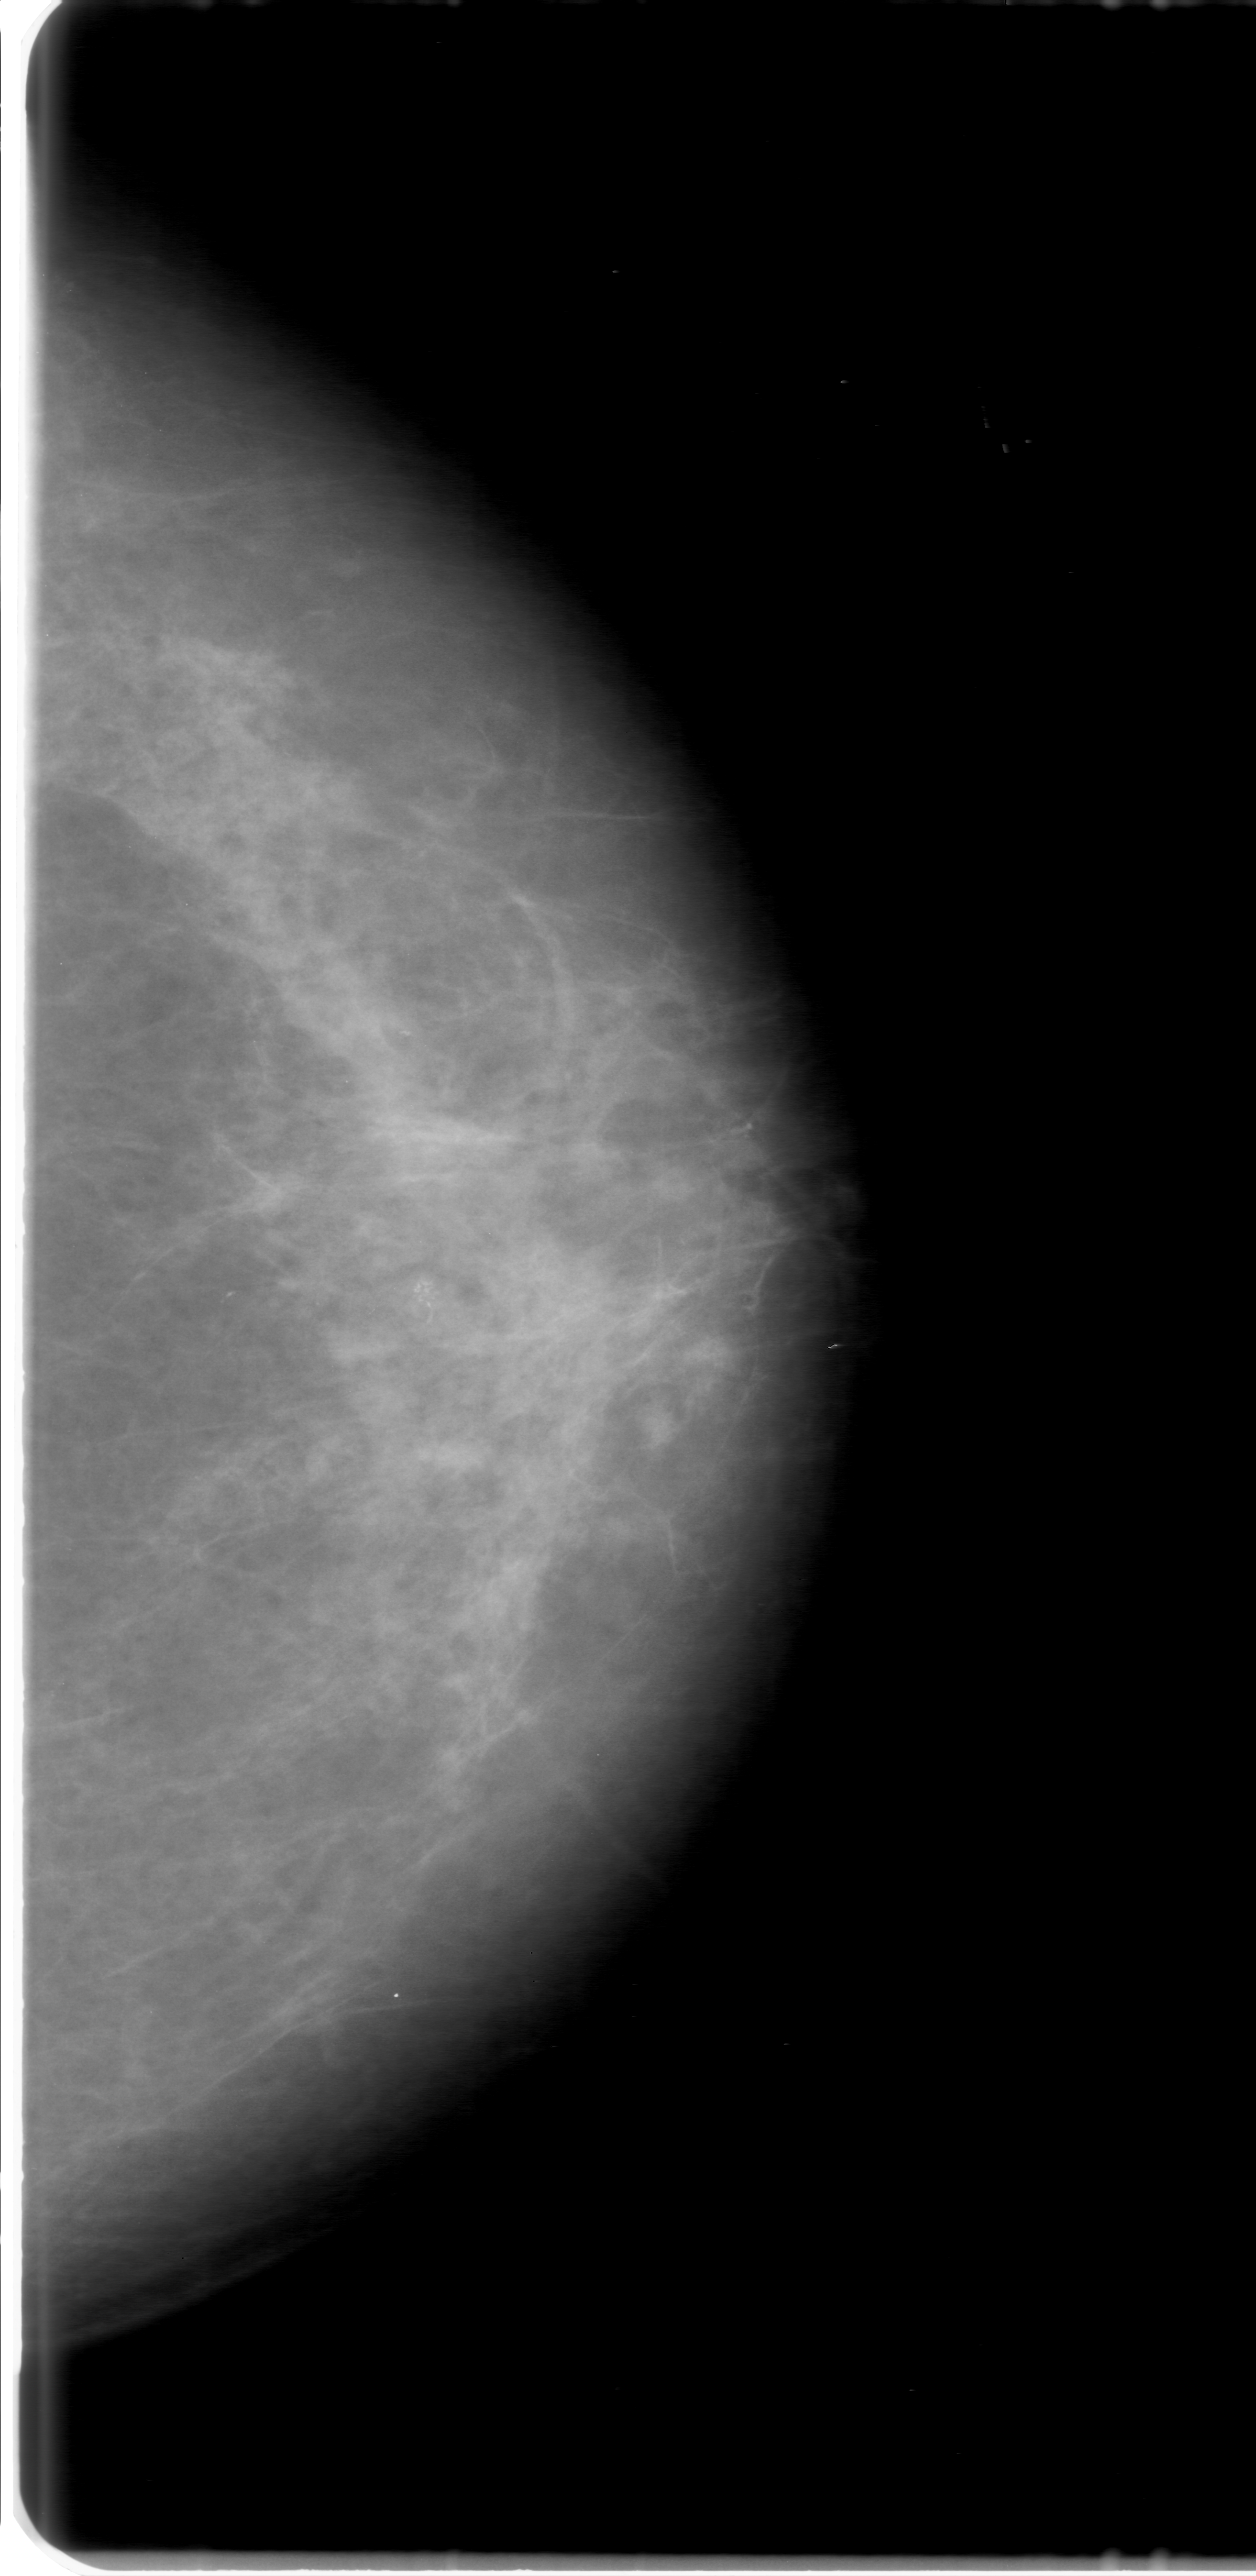
Mammogram (digitized film); left breast; craniocaudal (CC) view; breast composition: scattered fibroglandular densities (BI-RADS density category 2 of 4).
- Marked findings (only marked abnormalities are described; nothing is implied about the rest of the image): calcifications, morphology pleomorphic, distribution clustered; BI-RADS assessment category 3; subtlety rating 3 on a 1 (subtle) to 5 (obvious) scale; pathology result (as recorded, not read from the image): malignant.